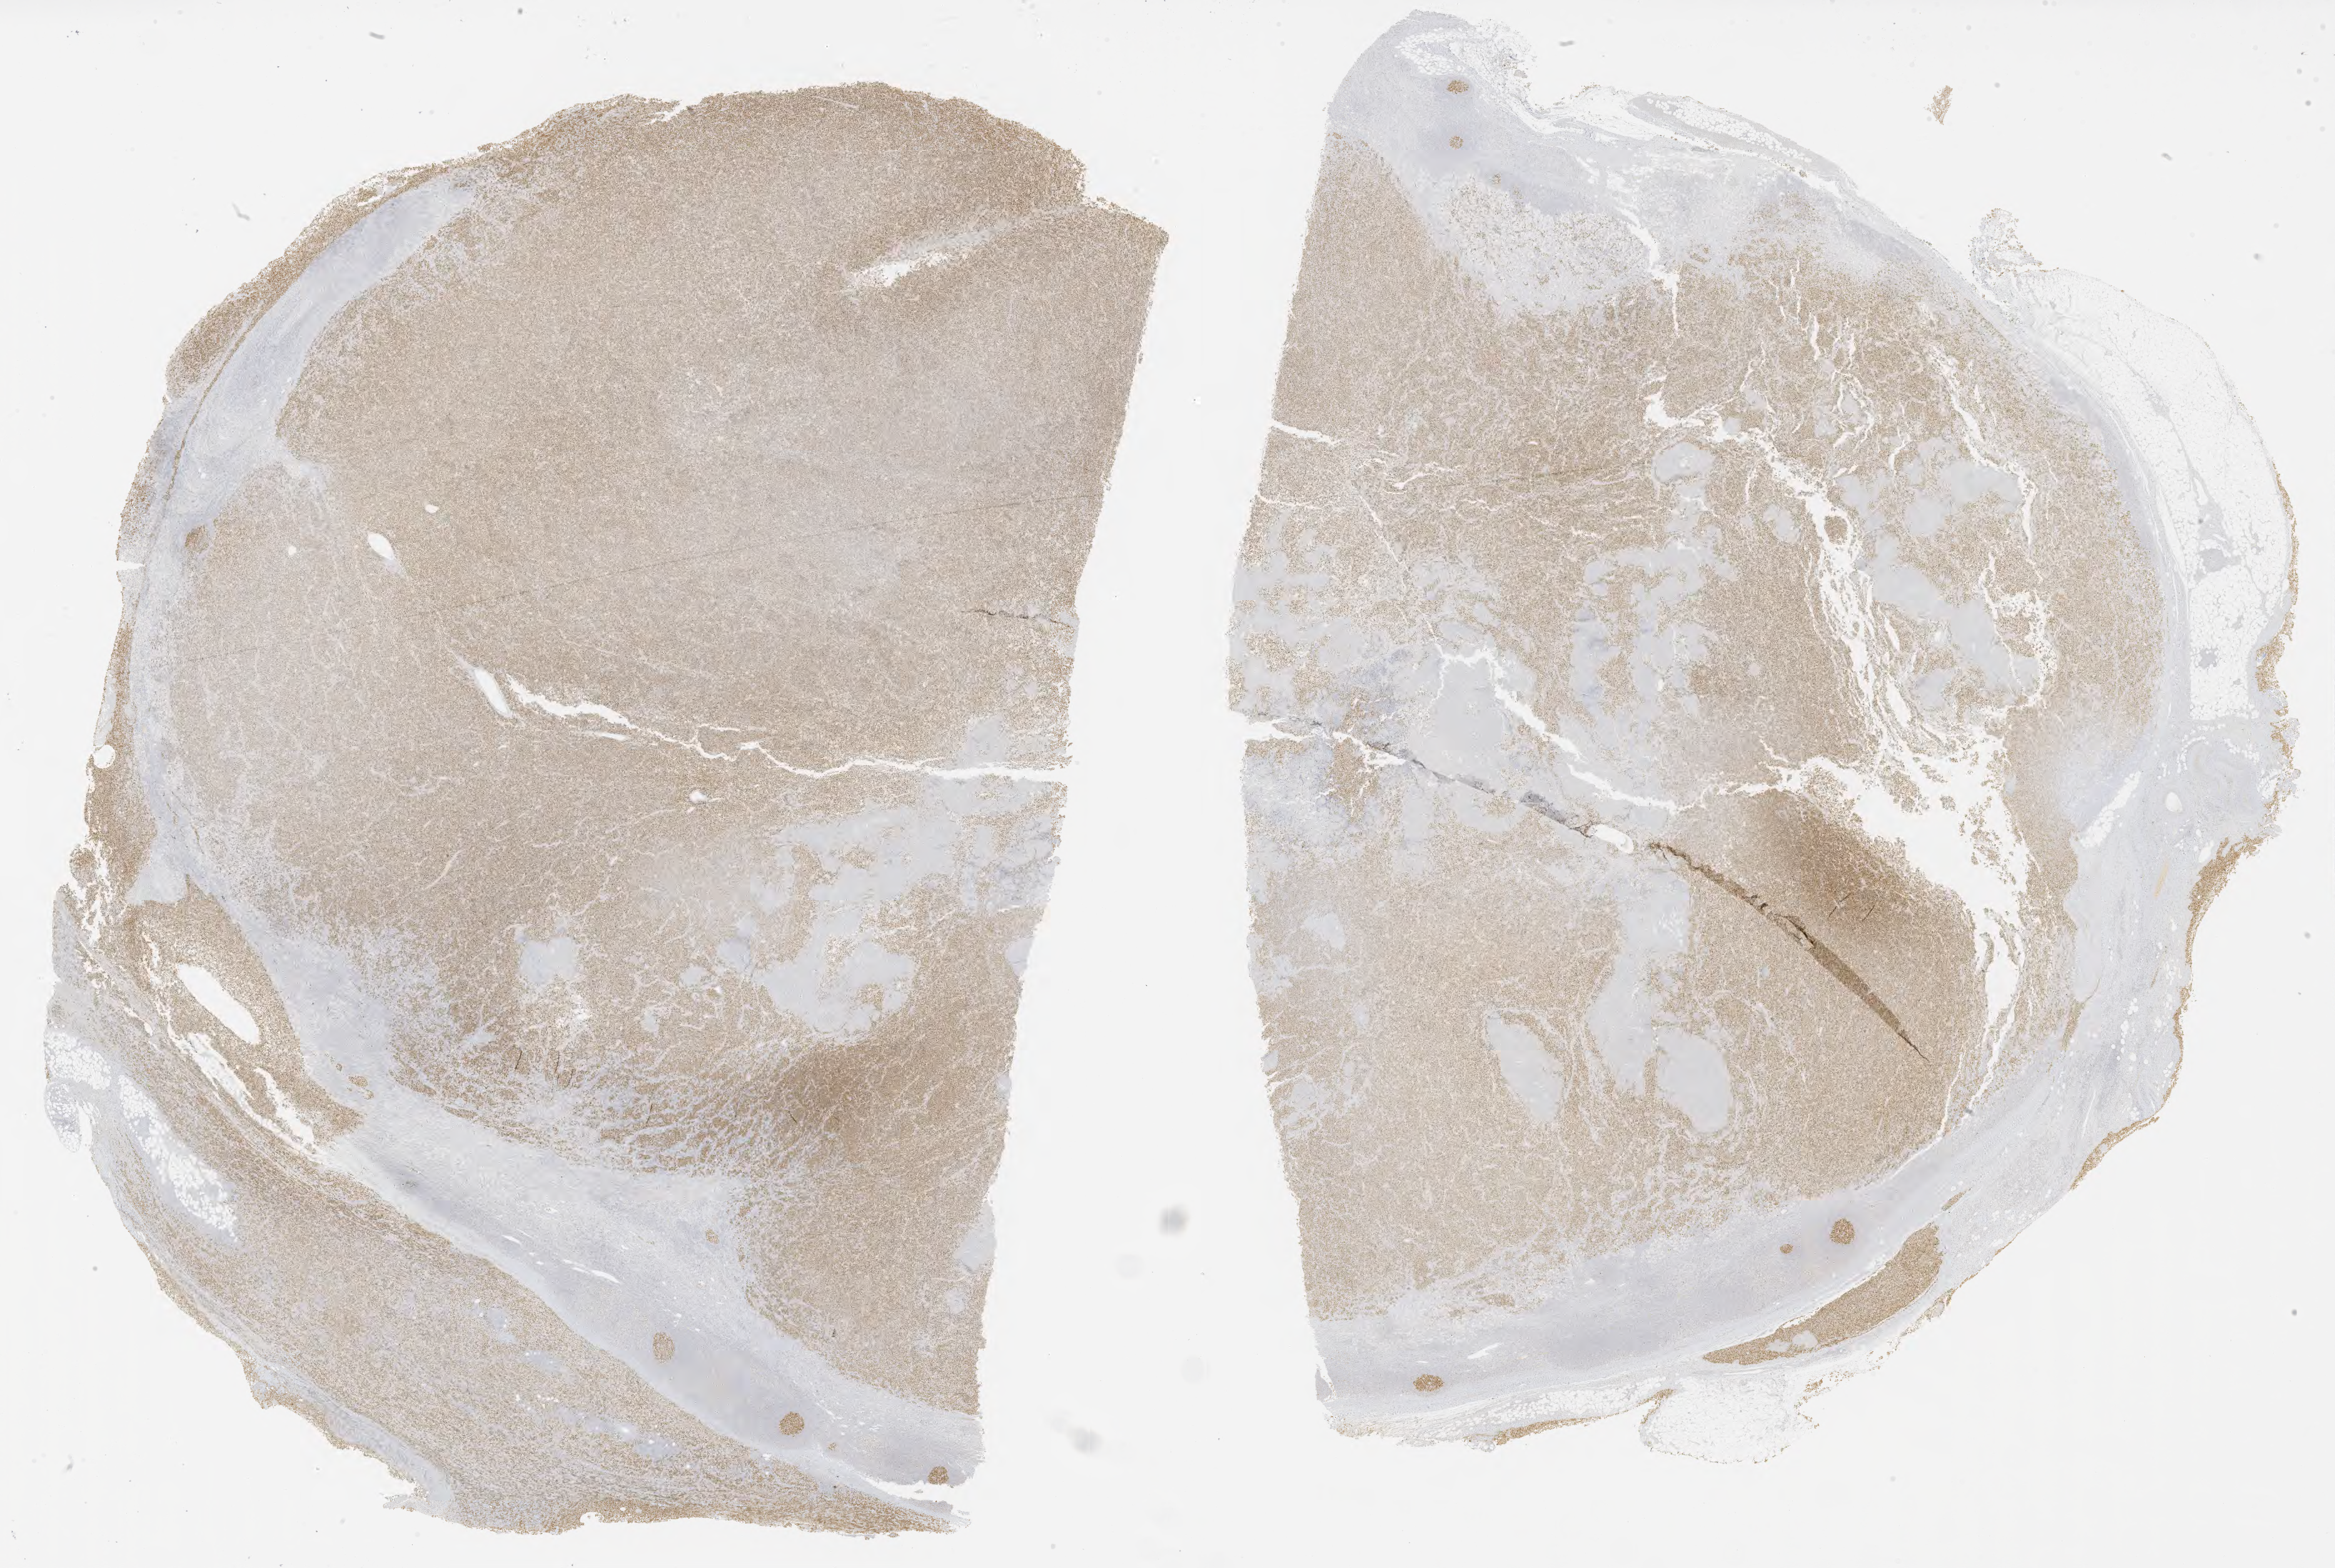
IHC for BCL6, whole-slide image, shown as a low-resolution overview of the whole scanned area (about 30.2 x 20.3 mm). Tumor tissue. Male patient, age 48 years.
Diagnosis: Burkitt lymphoma, NOS.